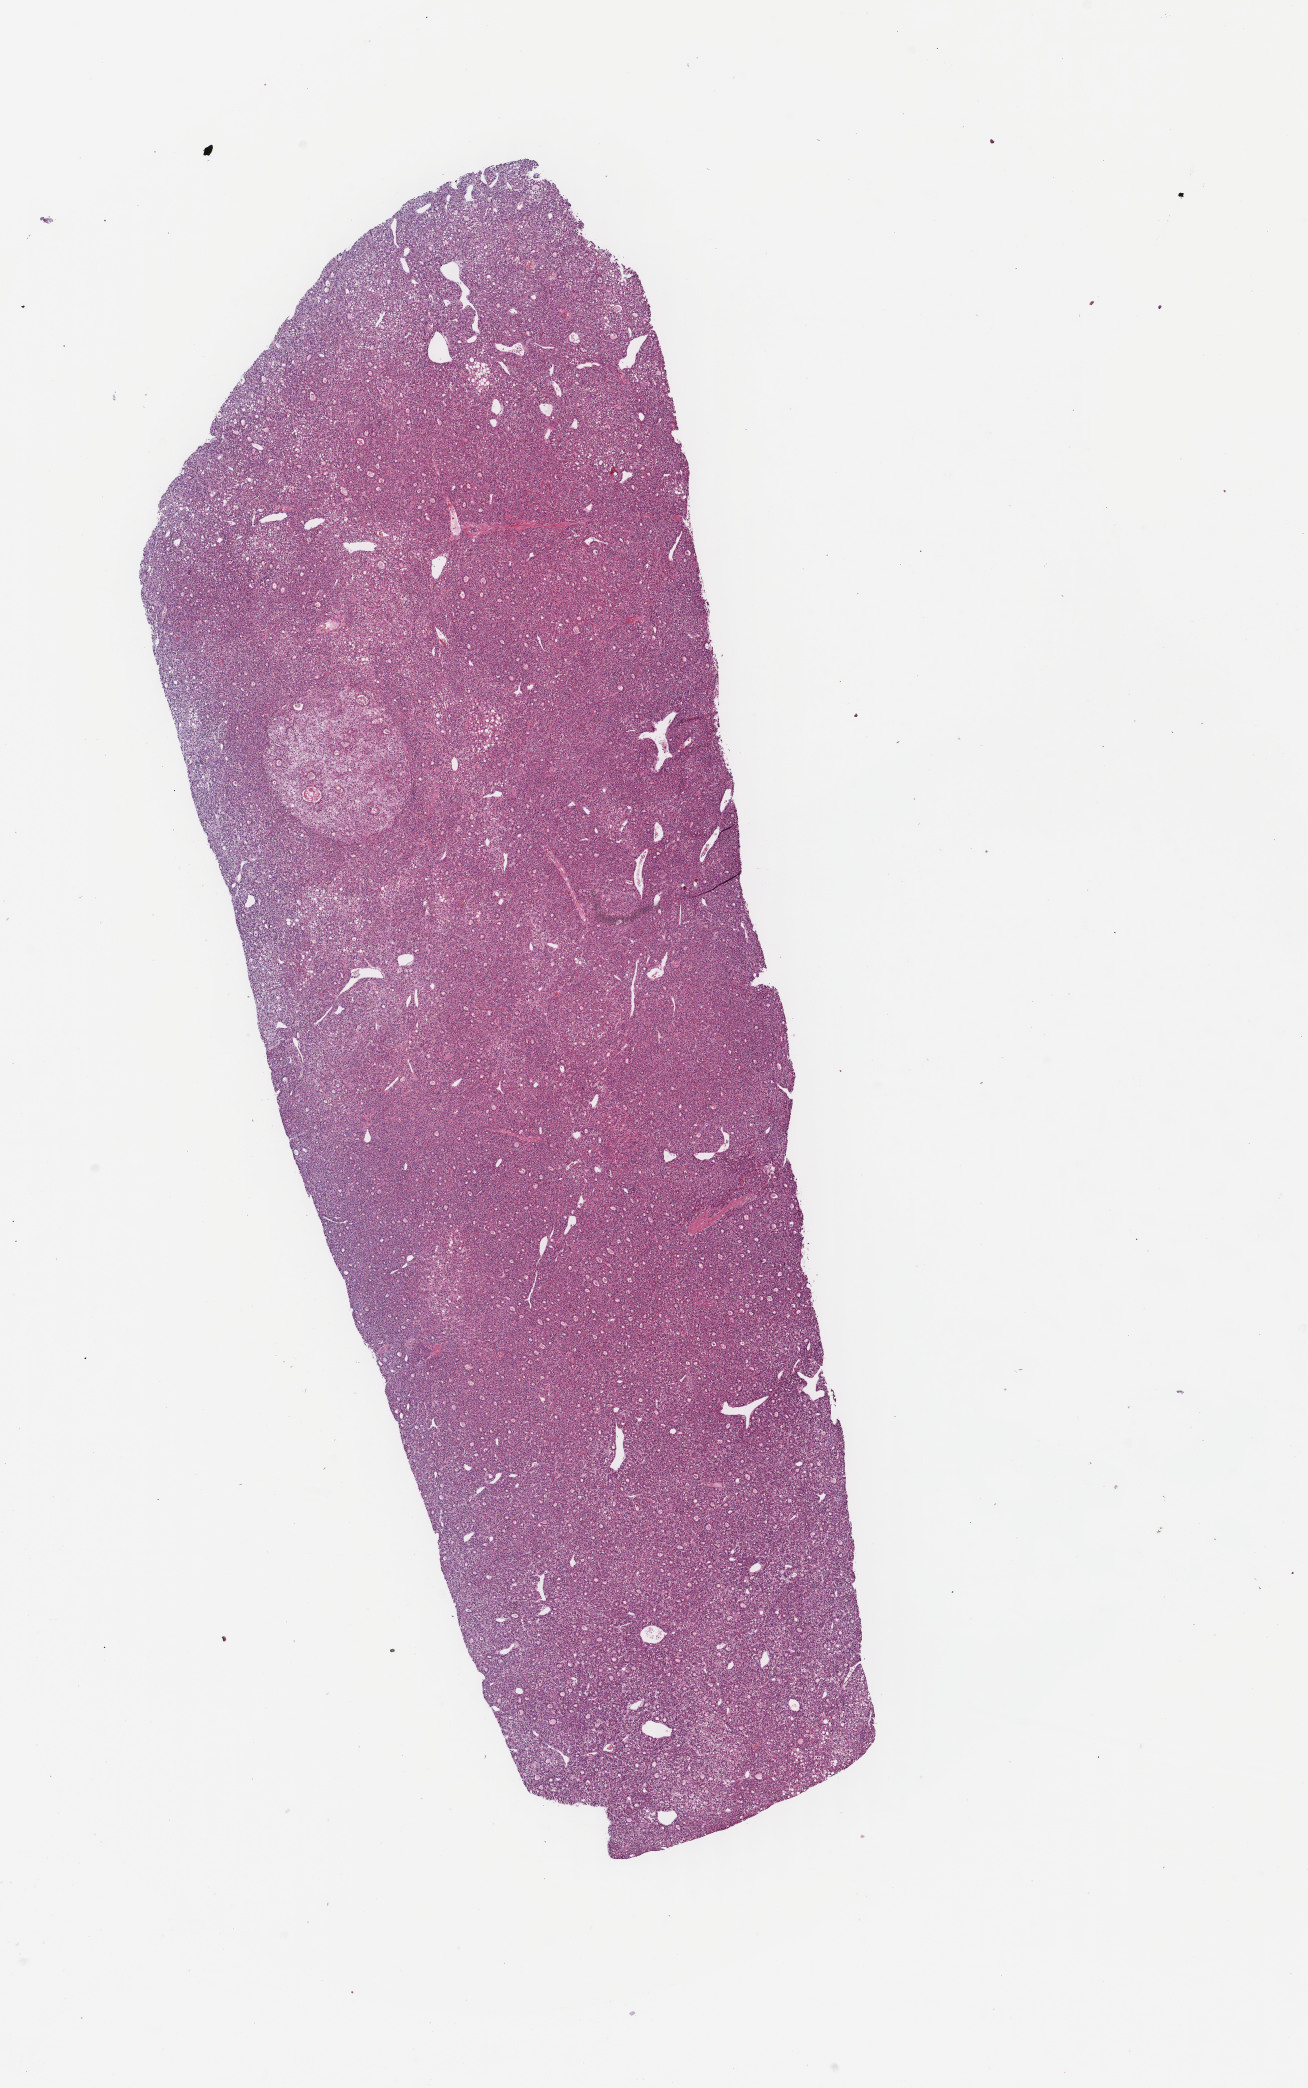
Digitized H&E tissue section (whole slide) — low-resolution overview of the scanned area, about 10.4 x 16.6 mm (acquisition: 40x scan), FFPE section, sample: primary tumour, liver. Male, age 70 years at initial diagnosis. Histologic grade: G2 (moderately differentiated).
- diagnosis: Hepatocellular carcinoma, NOS
- TNM: T1 N0 MX
- AJCC pathologic stage: I